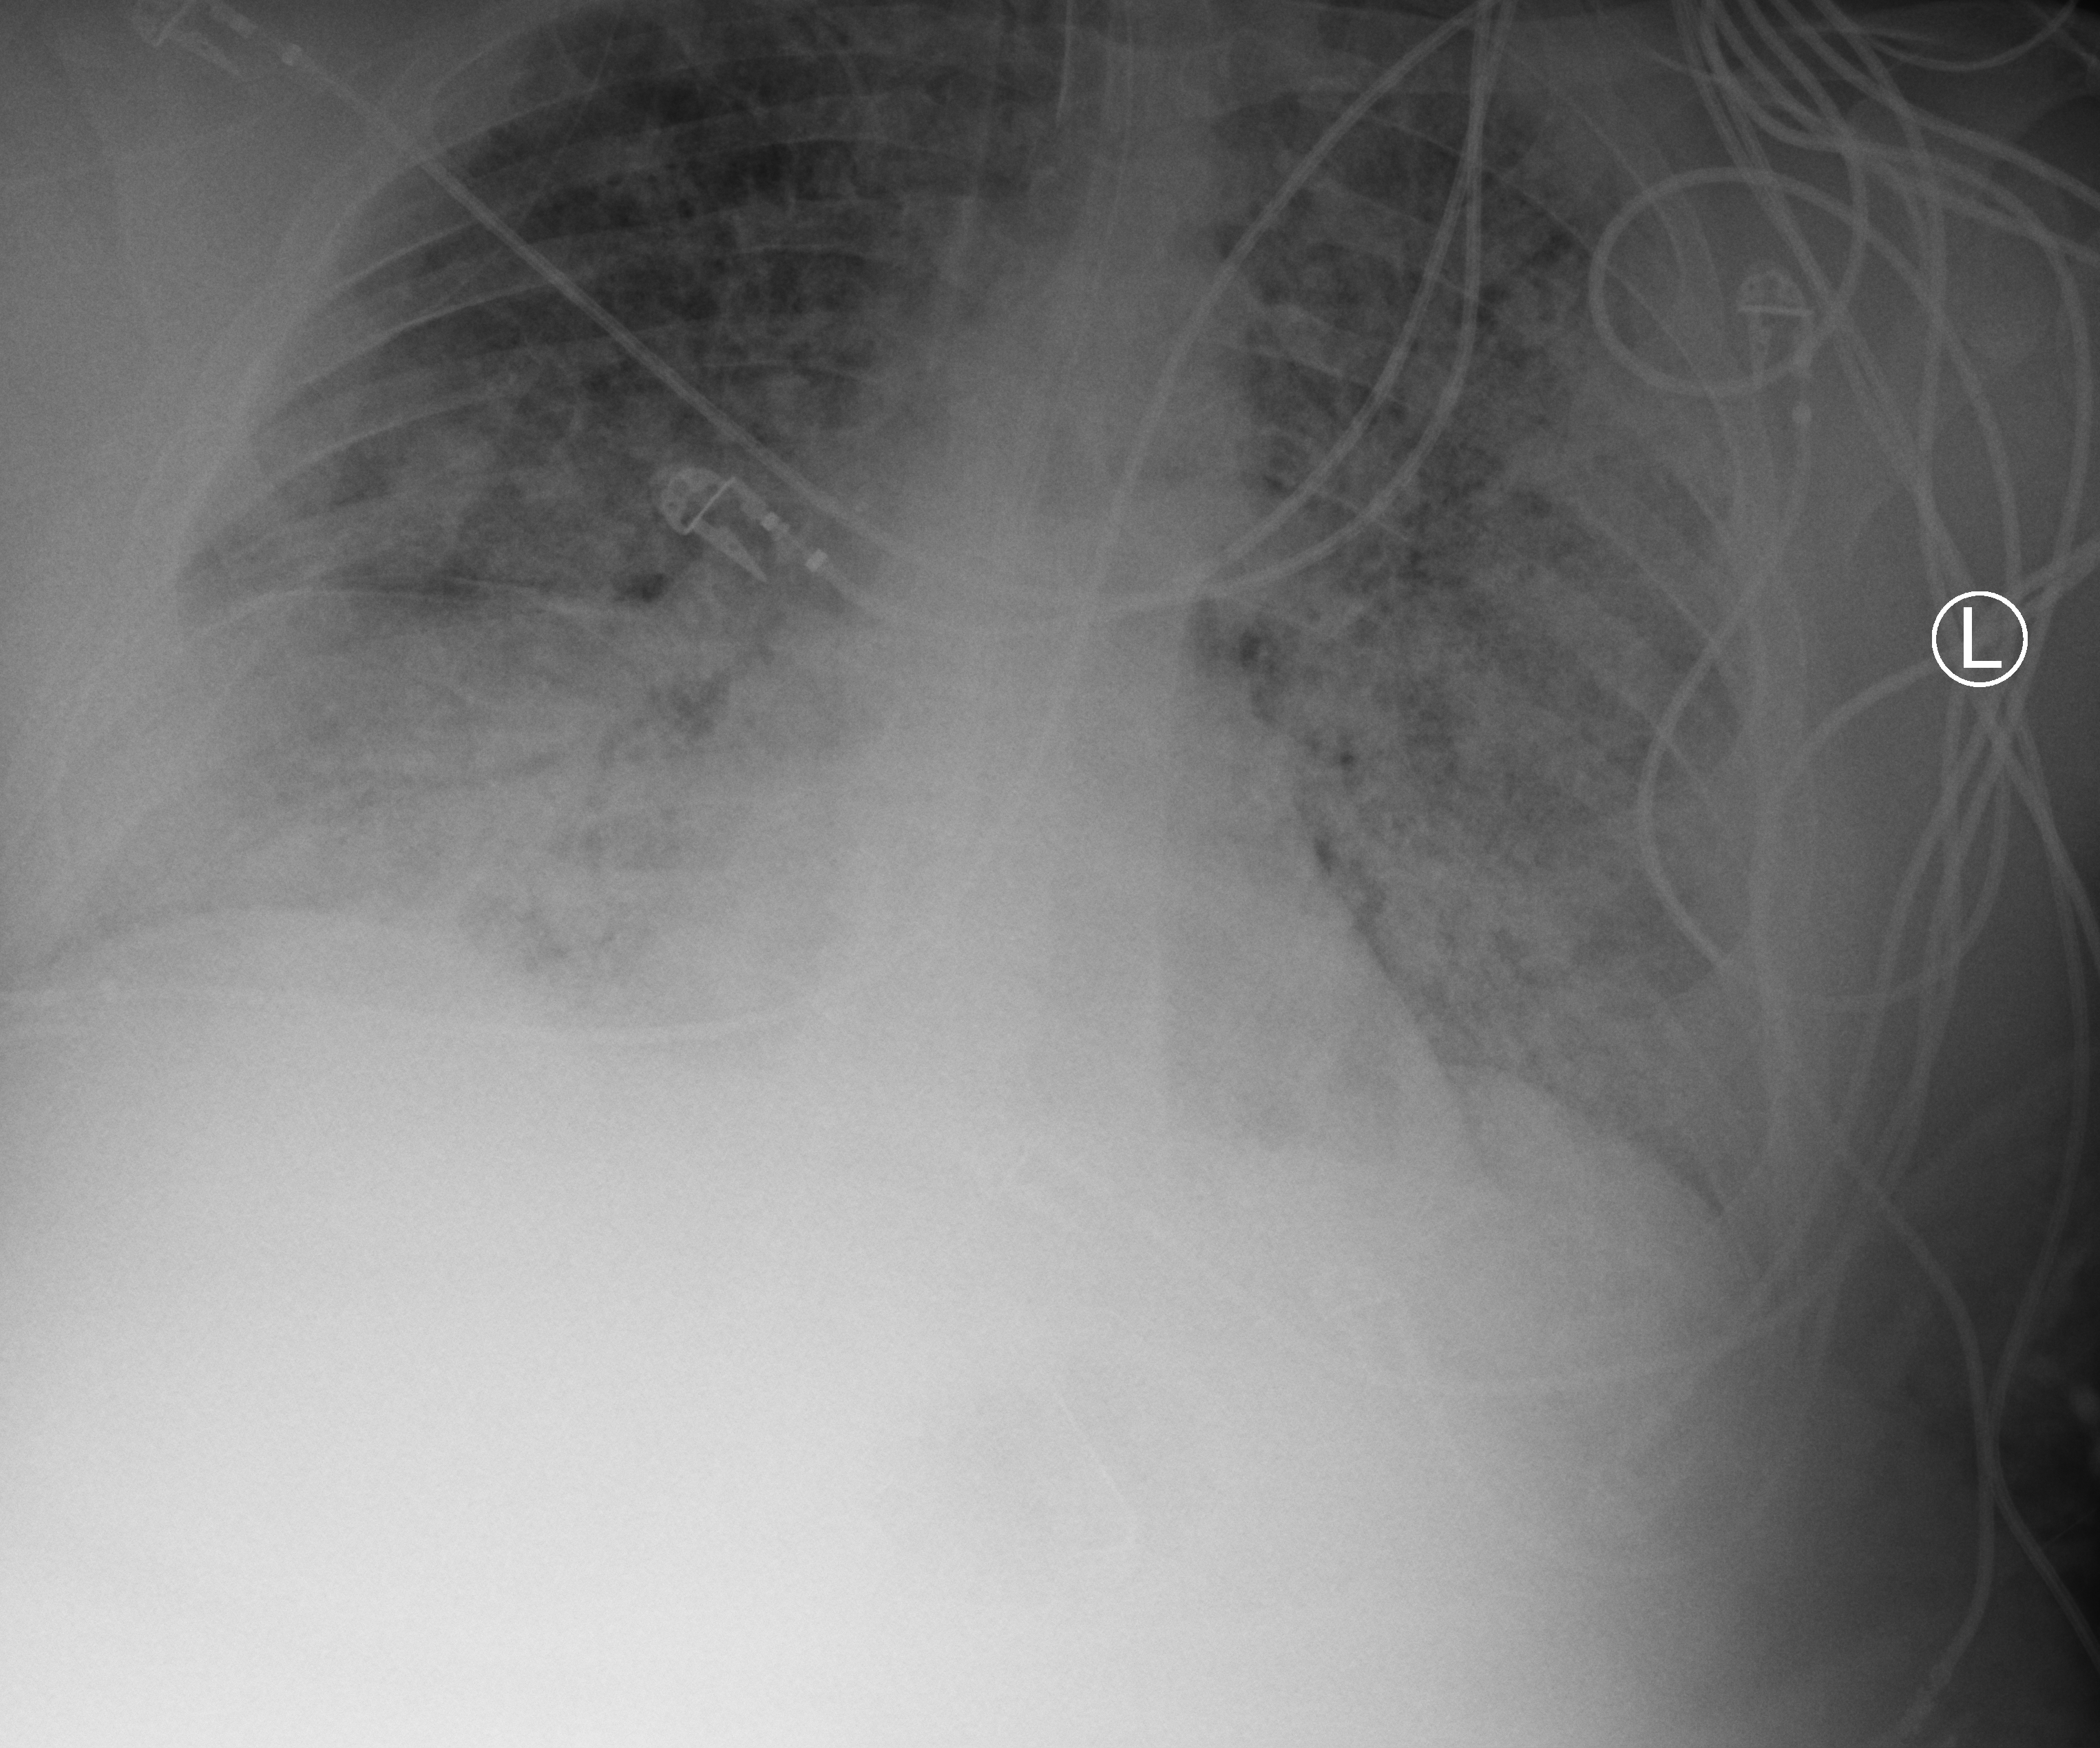
Chest X-ray (portable). Patient hospitalised with COVID-19; male, aged 60–74 years.
Hospital-stay facts (about this admission, not read from this image; timing relative to this image not recorded):
- length of hospital stay: 13 days
- admitted to intensive care during this hospital stay: yes
- mechanically ventilated during this hospital stay: yes